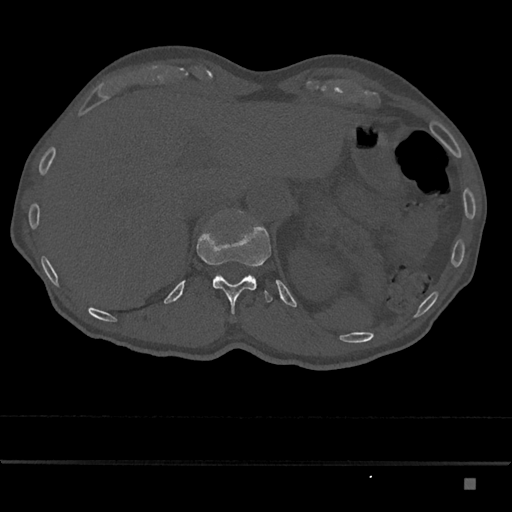
CT including the spine, one axial slice; slice 606 of 797 in the series (ordered by position); reconstruction kernel Br40s/3; 120 kVp; bone window (W 1800 / L 400 HU); 0.5 mm slice thickness; 512 × 512 image matrix, field of view 390 × 390 mm. Patient: male, 72 years. Case-level facts recorded for this patient, not image findings: primary cancer: prostate.
Annotated regions visible in this slice (semi-automatic segmentation, software-assisted and operator-edited):
- T12 vertebra: bounding box [x1, y1, x2, y2] px = [197, 226, 273, 315]